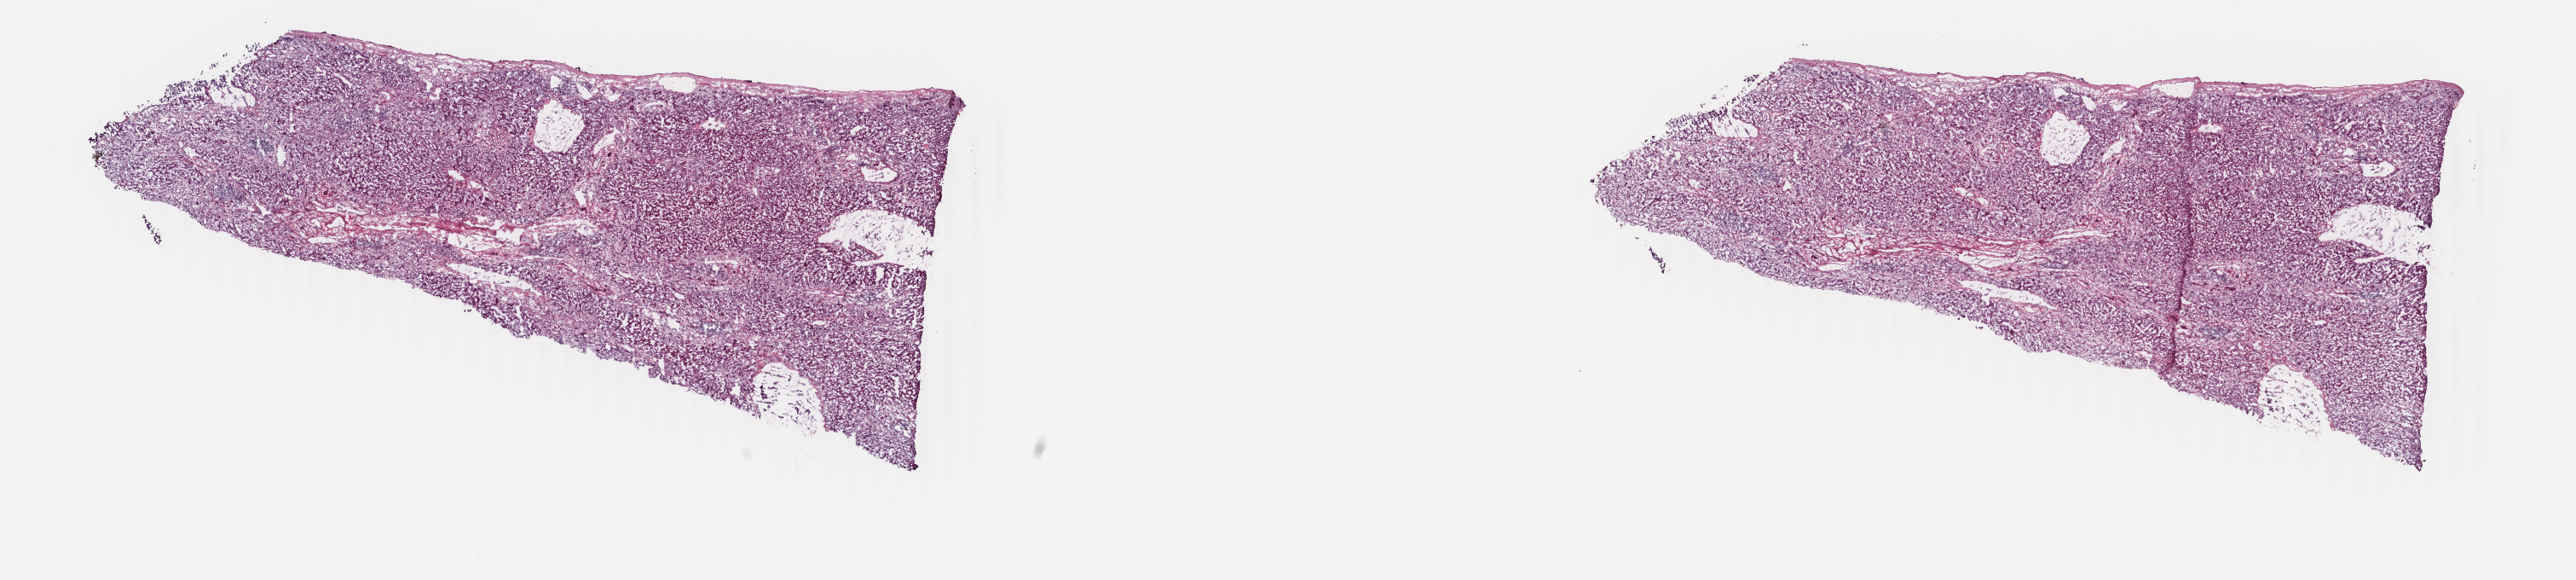
Digitized H&E tissue section (whole slide), a low-resolution overview of the entire scanned area, about 24.0 x 5.4 mm. Frozen section from the top of the tissue portion. Primary tumour sample from the liver. Patient: male, age at initial diagnosis 74 years. Histologic grade: G2 (moderately differentiated). Slide review estimates, as recorded: tumour cells 80%, tumour nuclei 65%, normal cells 20%, stromal cells 0%, necrosis 0%. Infiltration values recorded for this section: lymphocyte infiltration 8%, monocyte infiltration 0%, neutrophil infiltration 0%.
AJCC pathologic stage: I (7th edition). Pathologic diagnosis: Hepatocellular carcinoma, NOS.